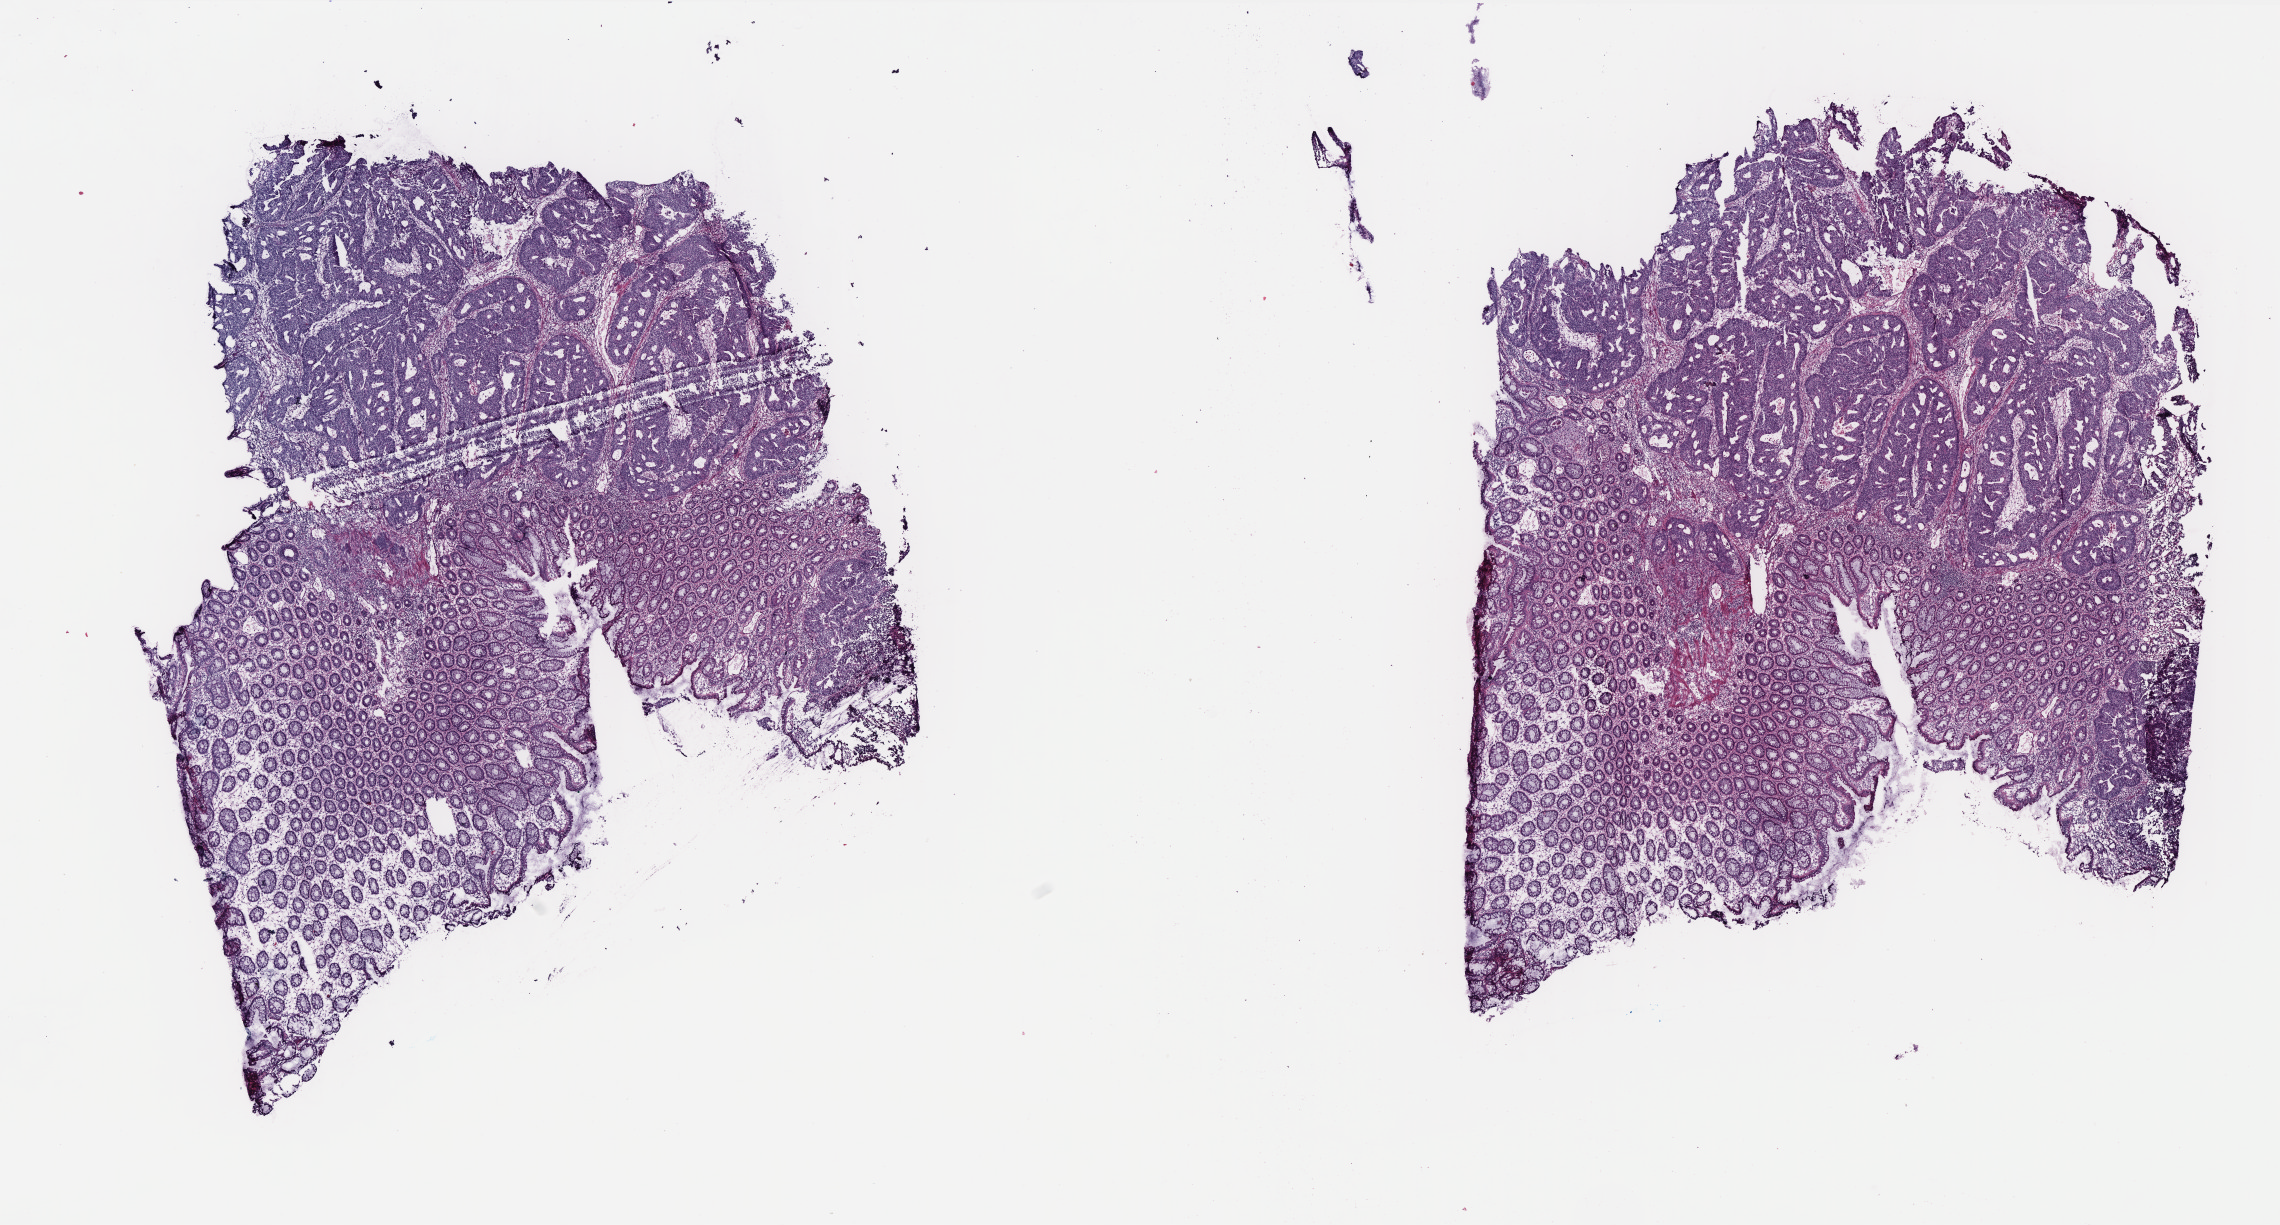
Digitized Hematoxylin and eosin (H&E) stained tissue section (whole slide), shown as a low-resolution overview of the whole scanned area (about 18.3 x 9.8 mm); frozen section; primary tumour sample from the rectum. Female patient; age at initial diagnosis 62 years. Composition of this section per pathologist review: tumour cells 55%, tumour nuclei 60%, normal cells 37%, stromal cells 5%, necrosis 3%. Infiltration values recorded for this section: lymphocyte infiltration 15%, monocyte infiltration 1%, neutrophil infiltration 1%.
- AJCC pathologic stage: I (5th edition)
- pathologic diagnosis: Adenocarcinoma, NOS
- lymph nodes positive (case pathology): 0 of 11 examined